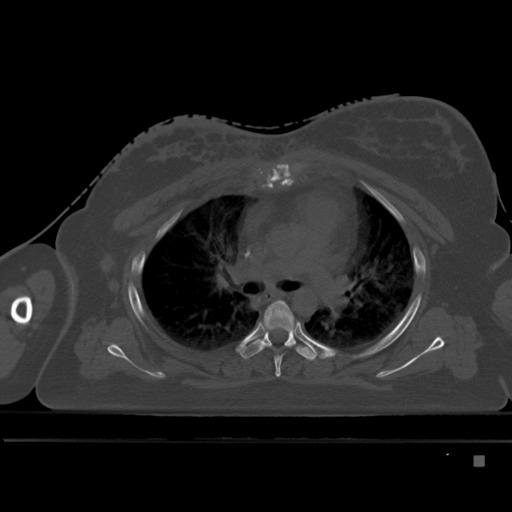
CT including the spine, one axial slice. Slice 325 of 495 in the series (ordered by position). Bone window (W 1800 / L 400 HU). 1.5 mm slice thickness. 512 × 512 image matrix, field of view 404 × 404 mm. Female patient, age 33 years. From the clinical record (not read from this slice): primary cancer: breast; vertebrae with lytic lesions (as recorded): T1.
Structures marked on this image (semi-automatic segmentation, software-assisted and operator-edited):
- T4 vertebra: bounding box (x1, y1, x2, y2) in pixels: (262, 300, 296, 377)
- T5 vertebra: (240, 326, 316, 361)